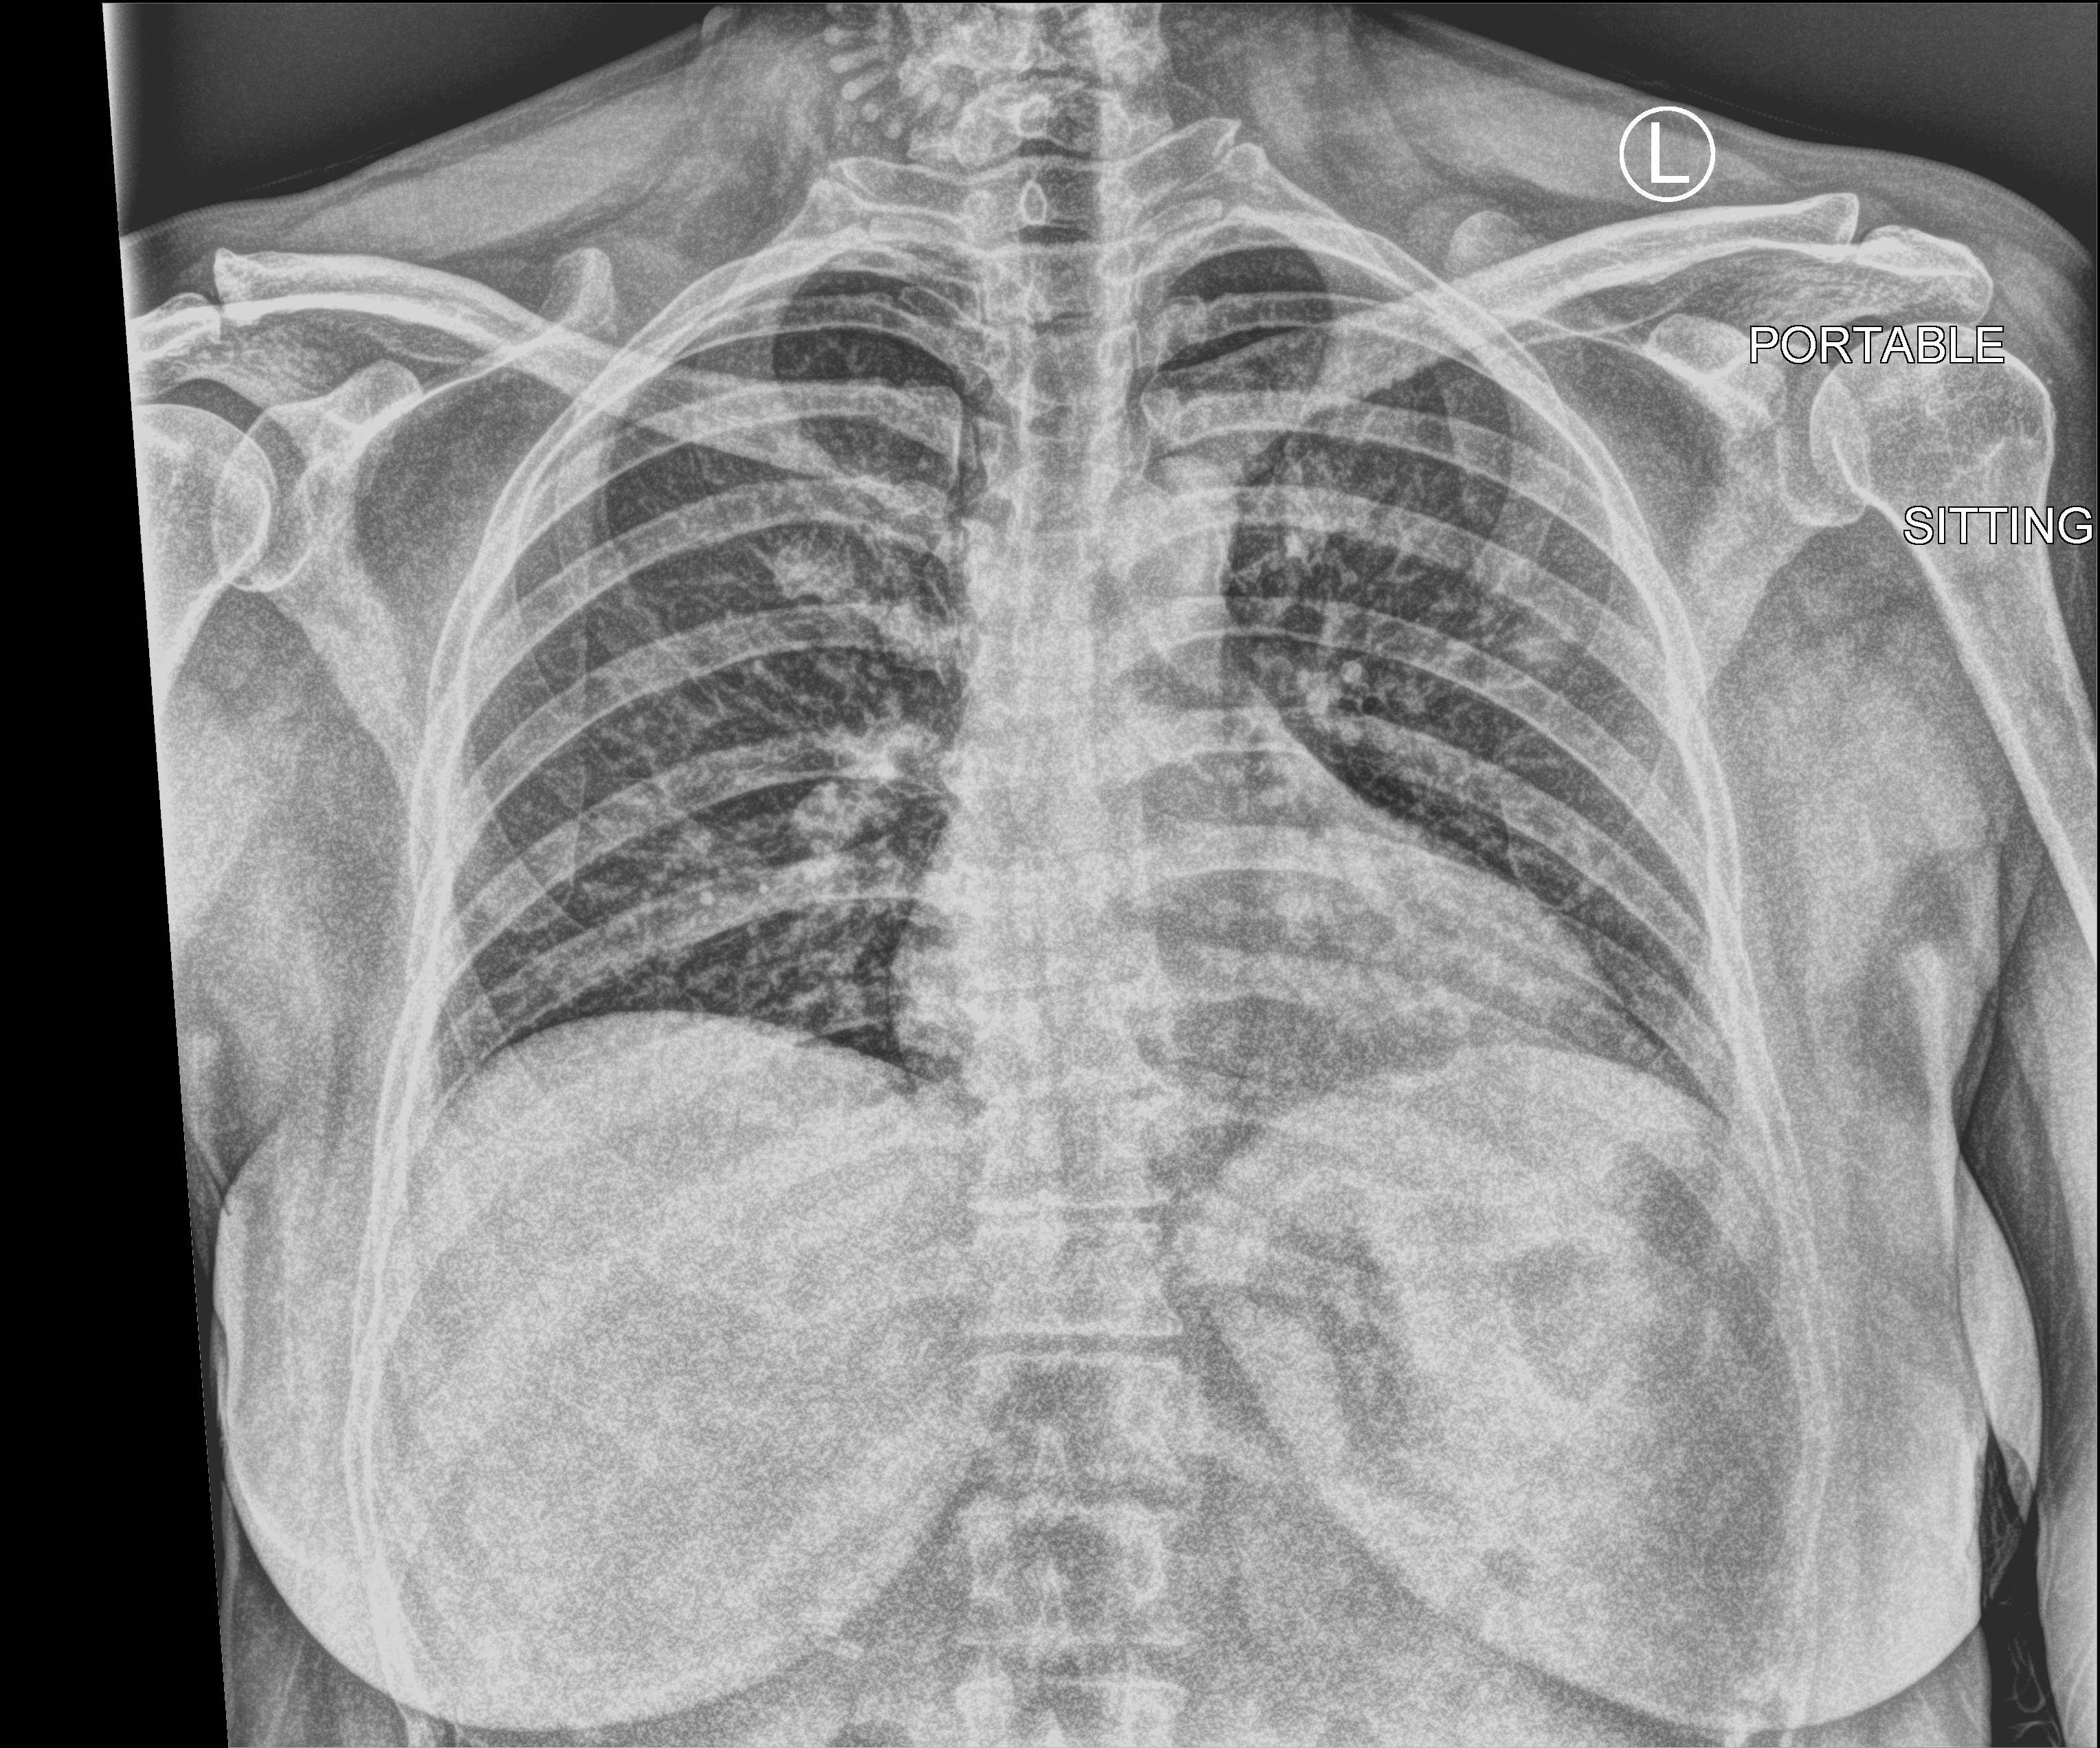
Chest X-ray (portable), anteroposterior (AP) projection. Patient hospitalised with COVID-19; female, aged 18–59 years.
Admission-level facts for this patient (not findings on this image; timing relative to this image not recorded): mechanically ventilated during this hospital stay: no; admitted to intensive care during this hospital stay: no.